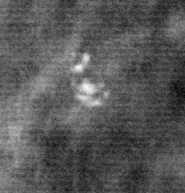
Crop from a digitized film mammogram around one marked abnormality, left breast, CC view, BI-RADS breast density category 1 (scale 1–4).
Marked abnormality: calcifications, morphology pleomorphic, distribution clustered; BI-RADS assessment category 4; subtlety rating 4 on a 1 (subtle) to 5 (obvious) scale; pathology result (as recorded, not read from the image): benign.